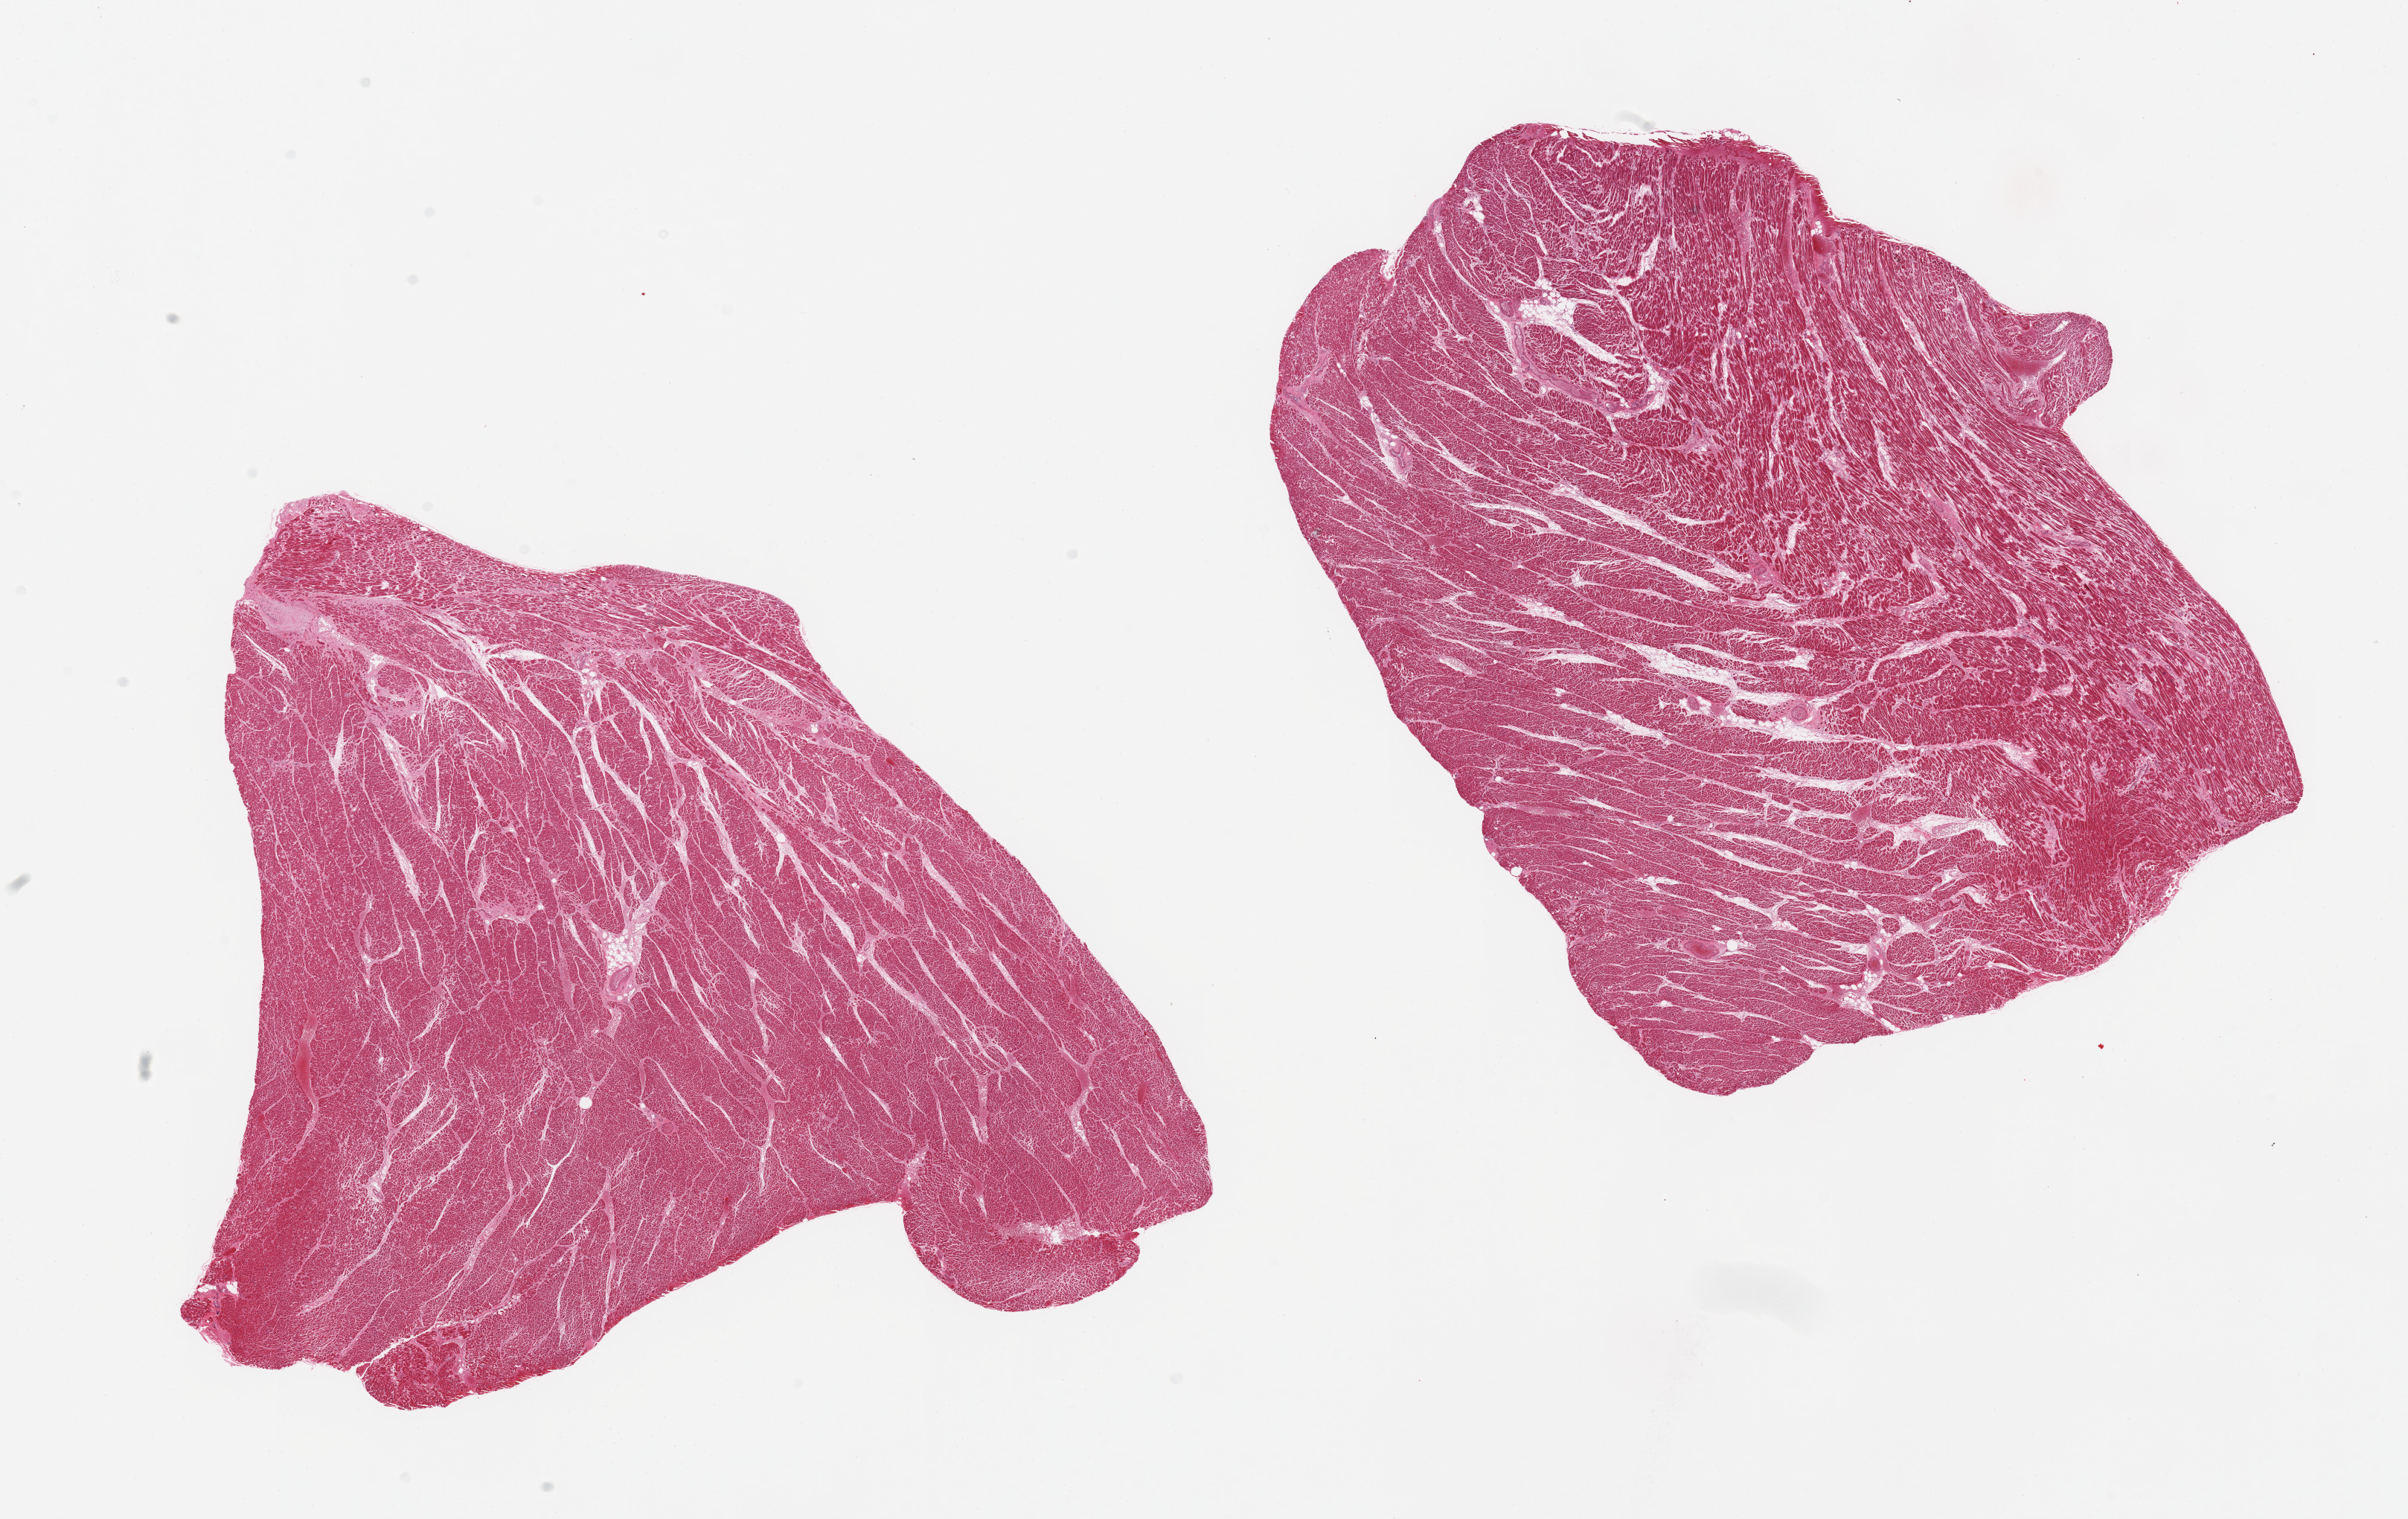
Haematoxylin and eosin whole-slide image, a low-resolution overview of the entire scanned area, about 25.6 x 16.1 mm; PAXgene-fixed paraffin-embedded (PFPE) section; section of heart (target tissue); donor tissue sample. Male donor.
- review note (as recorded): 2 pieces, minimal interstitial fibrosis